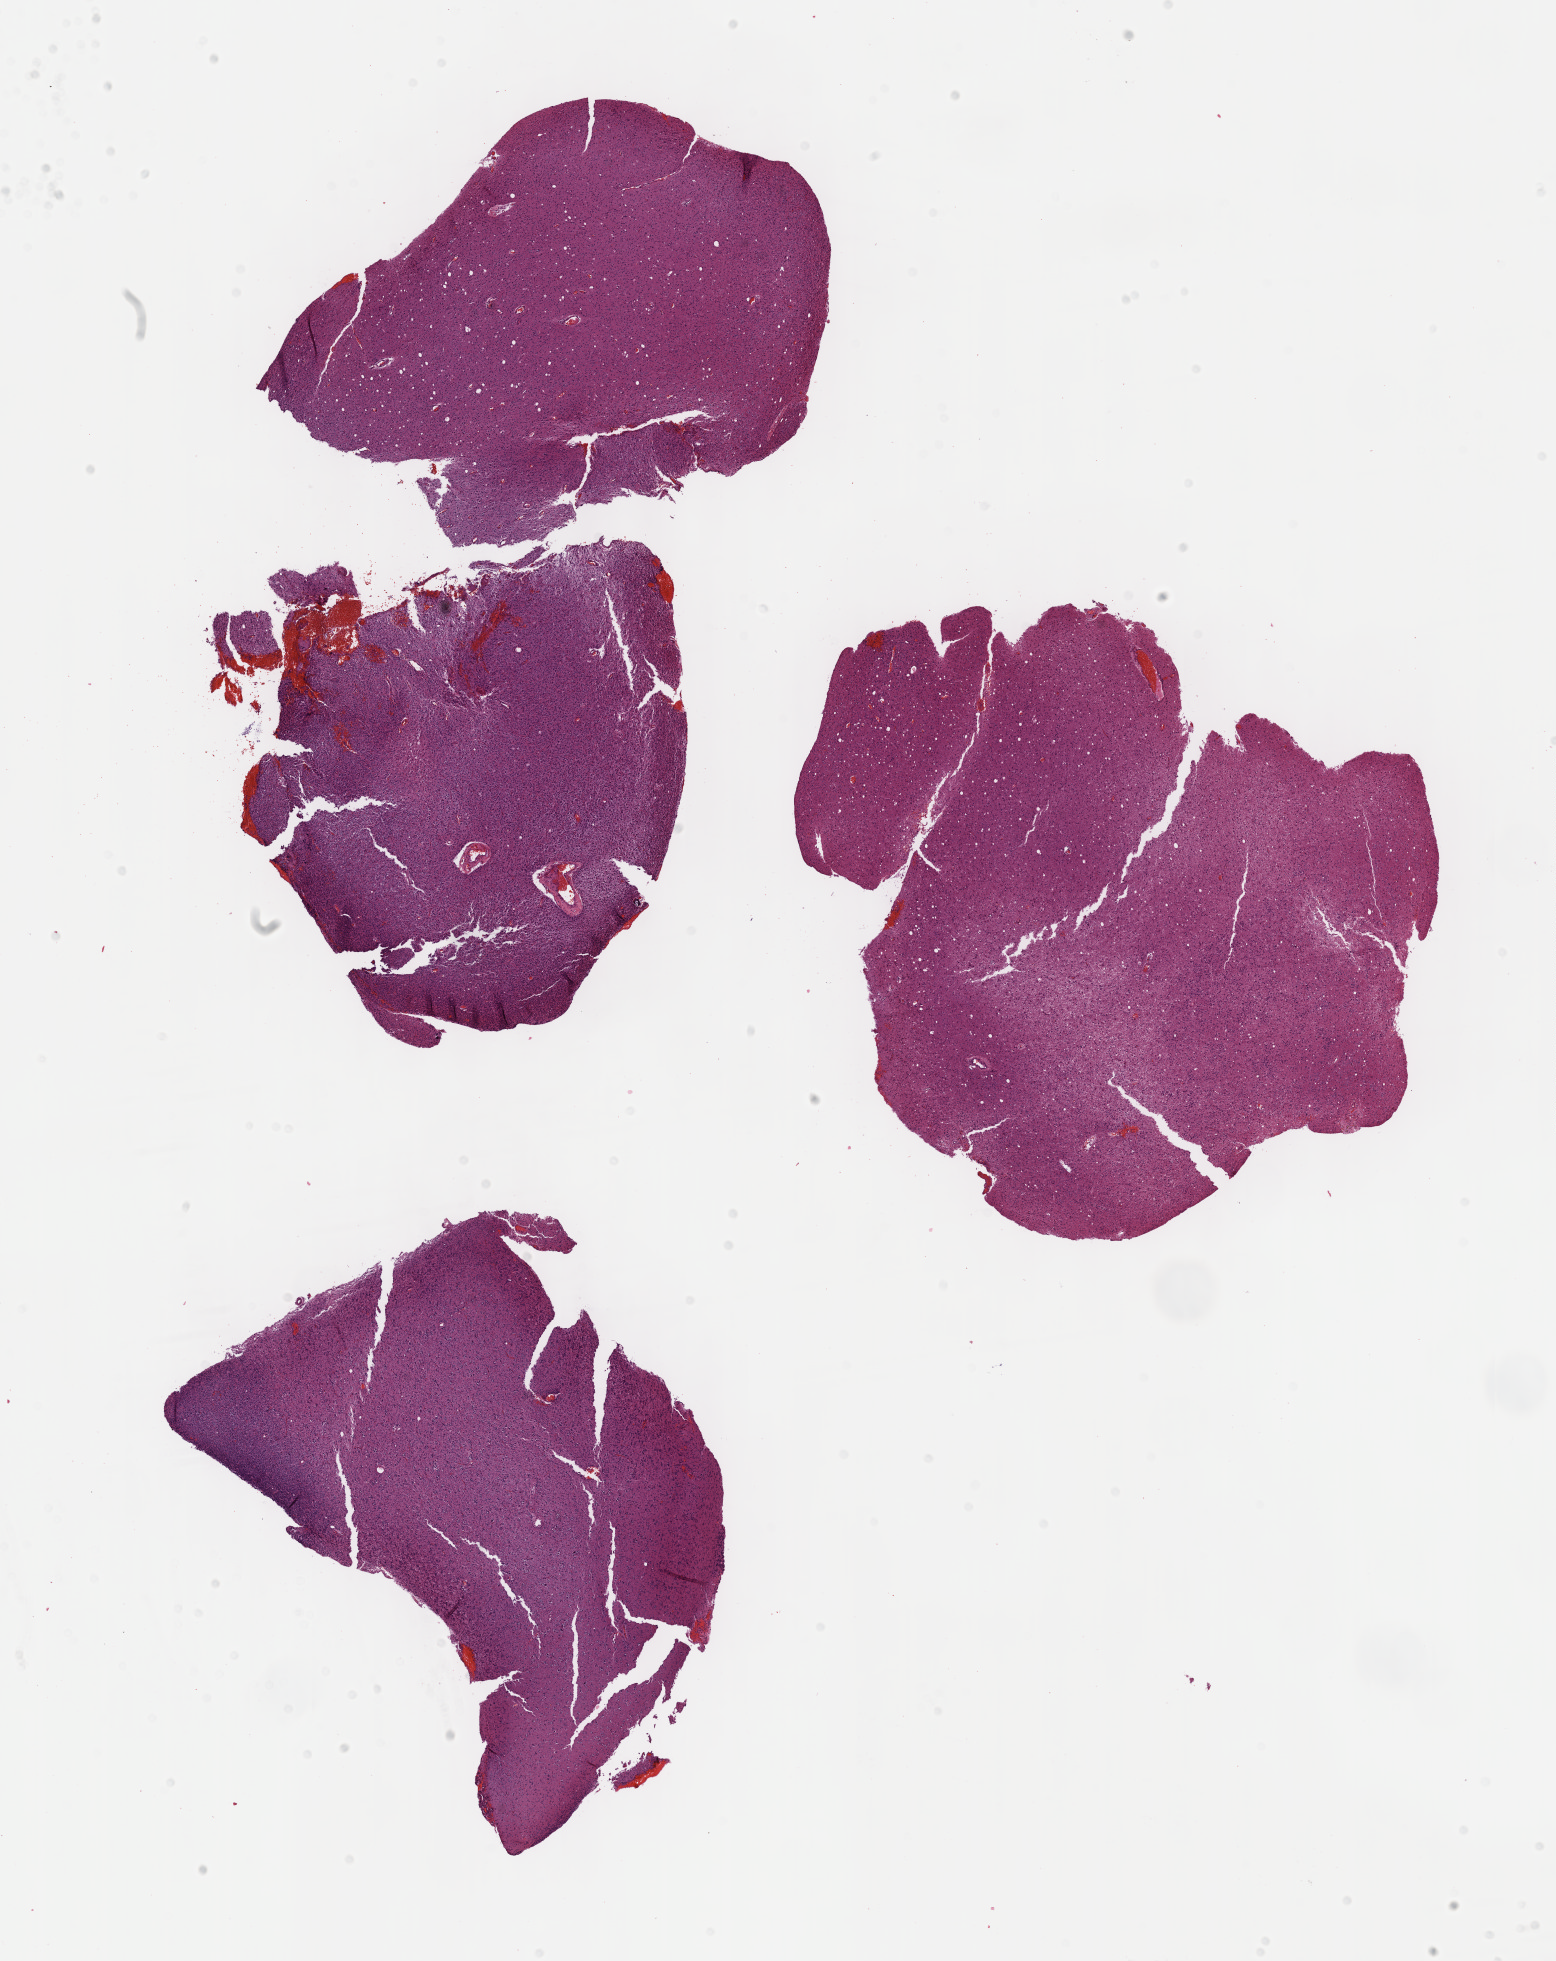
Digitized Hematoxylin and eosin (H&E) stained tissue section (whole slide), whole scanned area (about 12.6 x 15.9 mm, from a 40x scan) shown as a low-resolution overview, FFPE section, sample: primary tumour, brain. Male patient; age at initial diagnosis 39 years. Histologic grade: G2 (moderately differentiated).
Histologic diagnosis: Oligodendroglioma, NOS.